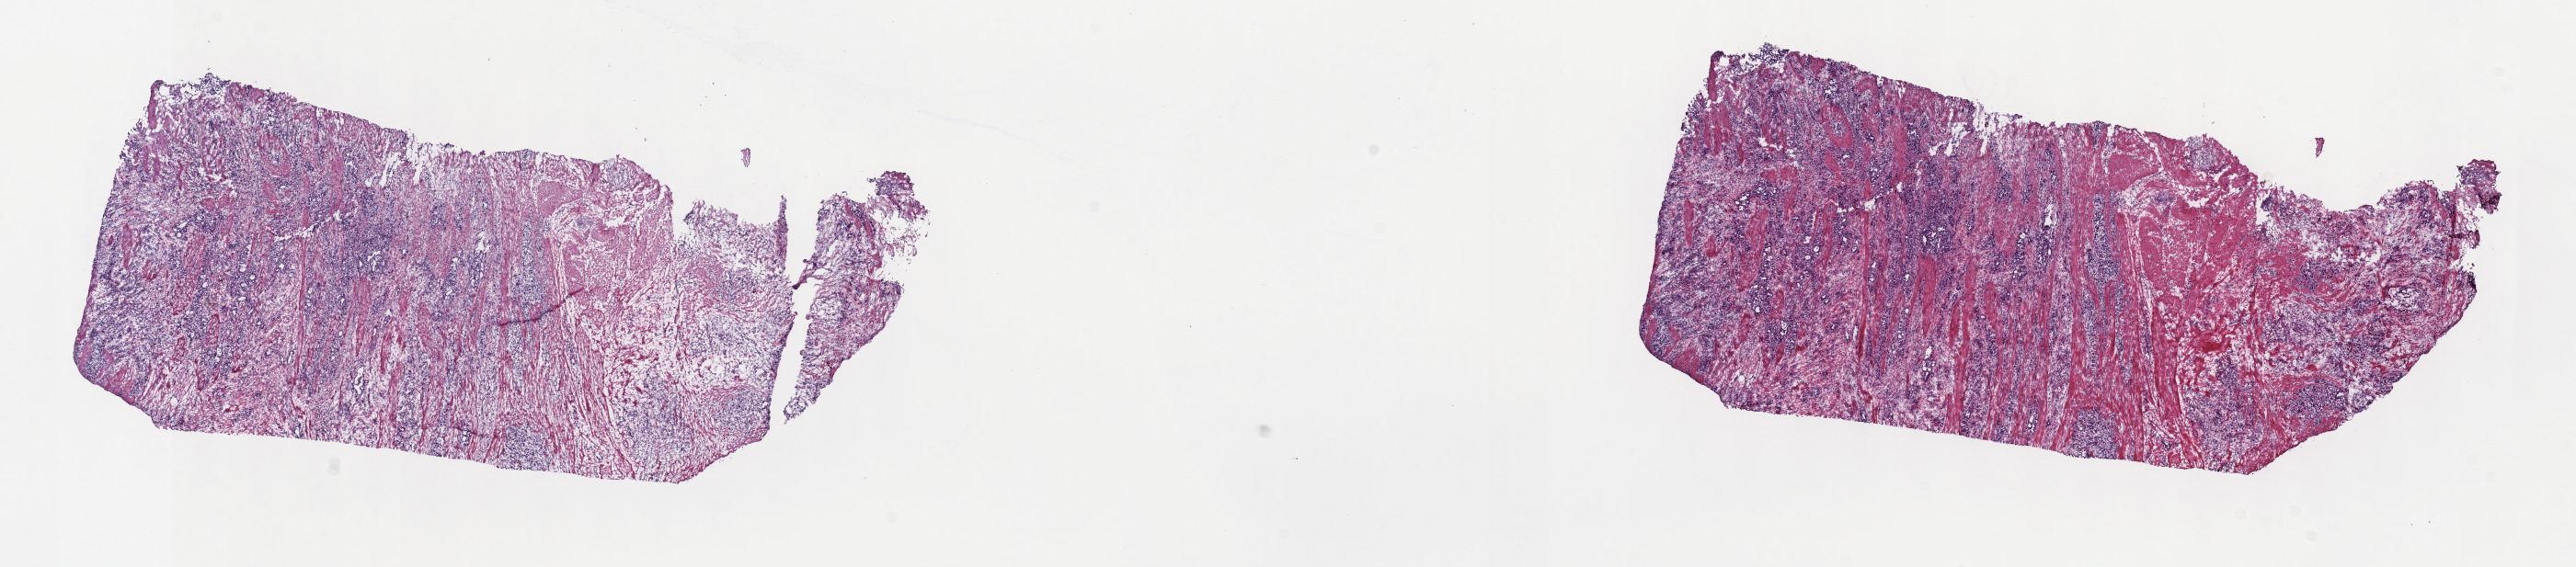
Hematoxylin and eosin (H&E) stained whole-slide image, a low-resolution overview of the entire scanned area, about 22.7 x 5.0 mm (acquisition: 40x scan); frozen section from the top of the tissue portion; sample: primary tumour, stomach. Patient: male, age at initial diagnosis 67 years. Histologic grade: G3 (poorly differentiated). Slide review estimates, as recorded: tumour cells 100%, tumour nuclei 60%, normal cells 0%, stromal cells 0%, necrosis 0%. Infiltration values recorded for this section: lymphocyte infiltration 4%, monocyte infiltration 0%, neutrophil infiltration 0%.
AJCC pathologic stage: IIIC (6th edition). Lymph nodes positive (case pathology): 50 of 60 examined. Pathologic diagnosis: Tubular adenocarcinoma (gastric antrum).